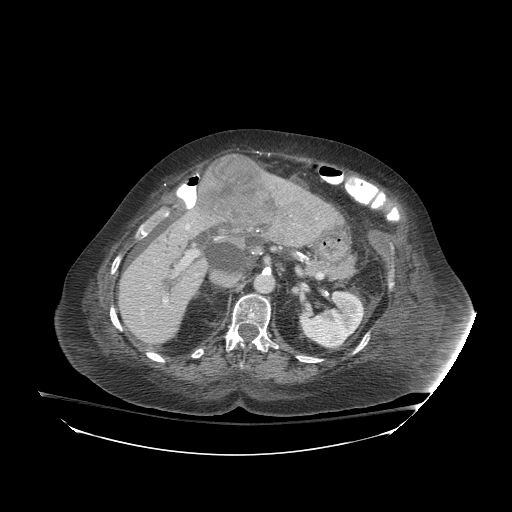
Contrast-enhanced abdominal CT (liver protocol), one axial slice; slice 46 of 81 in the series (ordered by position); soft-tissue window (W 400 / L 40 HU); 2.5 mm slice thickness; 512 × 512 image matrix. Case-level facts recorded for this patient, not image findings: diagnosis: hepatocellular carcinoma (patient treated with transarterial chemoembolisation; whether this scan precedes or follows treatment is not stated here); TNM stage (as recorded): Stage-I; Child-Pugh class: B; tumour differentiation: well-moderately differentiated.
Structures marked on this image (semi-automatic segmentation, software-assisted and operator-edited):
- liver parenchyma outside the tumour (the mass and vessels are separate outlines, so this box may not span the whole liver): box from (x=118, y=177) to (x=342, y=344) px
- mass: (x=200, y=155)–(x=276, y=226)
- liver vessels: (x=148, y=224)–(x=198, y=303)